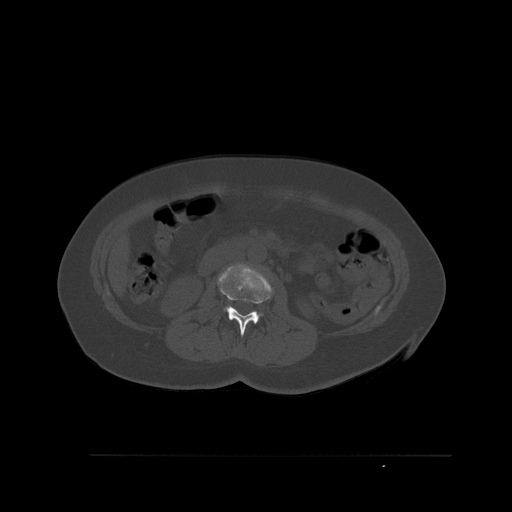
CT including the spine, one axial slice. Slice 243 of 527 in the series (ordered by position). Bone window (W 1800 / L 400 HU). 1.5 mm slice thickness. 512 × 512 image matrix, field of view 470 × 470 mm. Patient: female, 73 years. Case-level facts recorded for this patient, not image findings: primary cancer: breast.
Annotated regions visible in this slice (semi-automatically segmented with operator editing):
- L2 vertebra: bounding box [x1, y1, x2, y2] px = [221, 262, 270, 336]